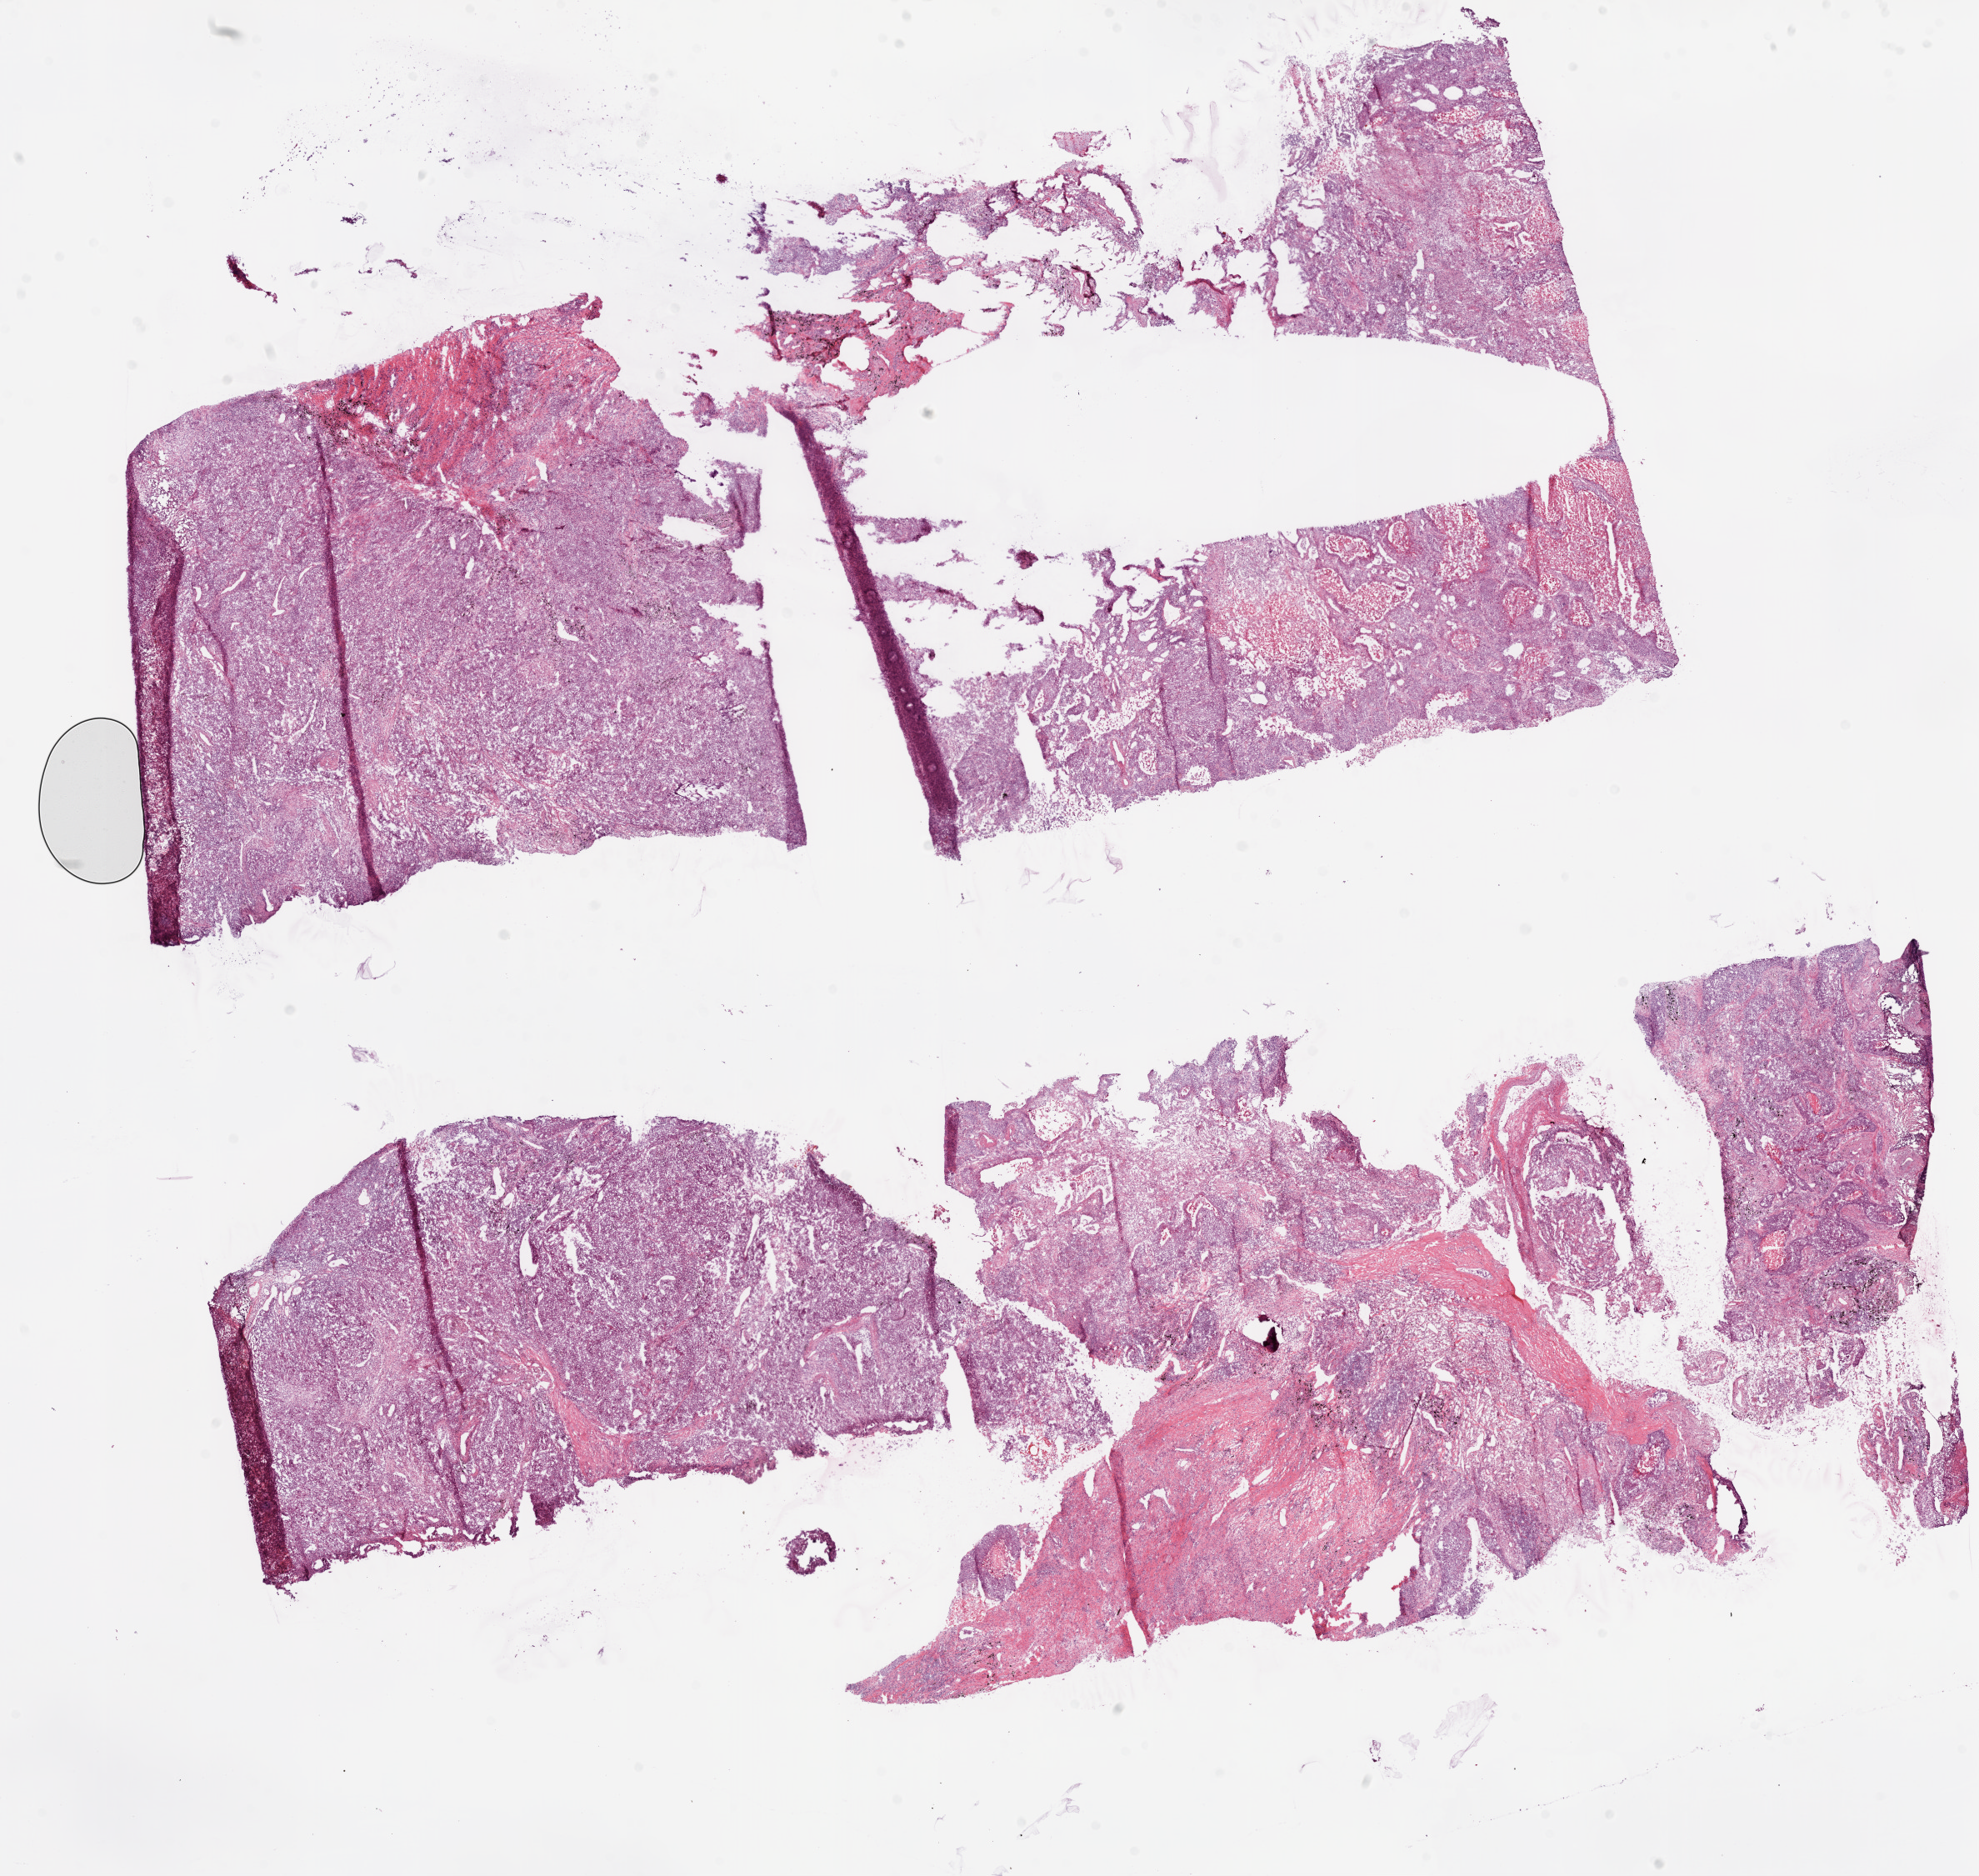
Digitized H&E tissue section (whole slide), shown as a low-resolution overview of the whole scanned area (about 19.1 x 18.1 mm); frozen section; sample: primary tumour, lung. Male patient; age at initial diagnosis 76 years. Pathologist review of this section (percent, as recorded): tumour cells 80%, tumour nuclei 65%.
Pathologic diagnosis: Squamous cell carcinoma, NOS.